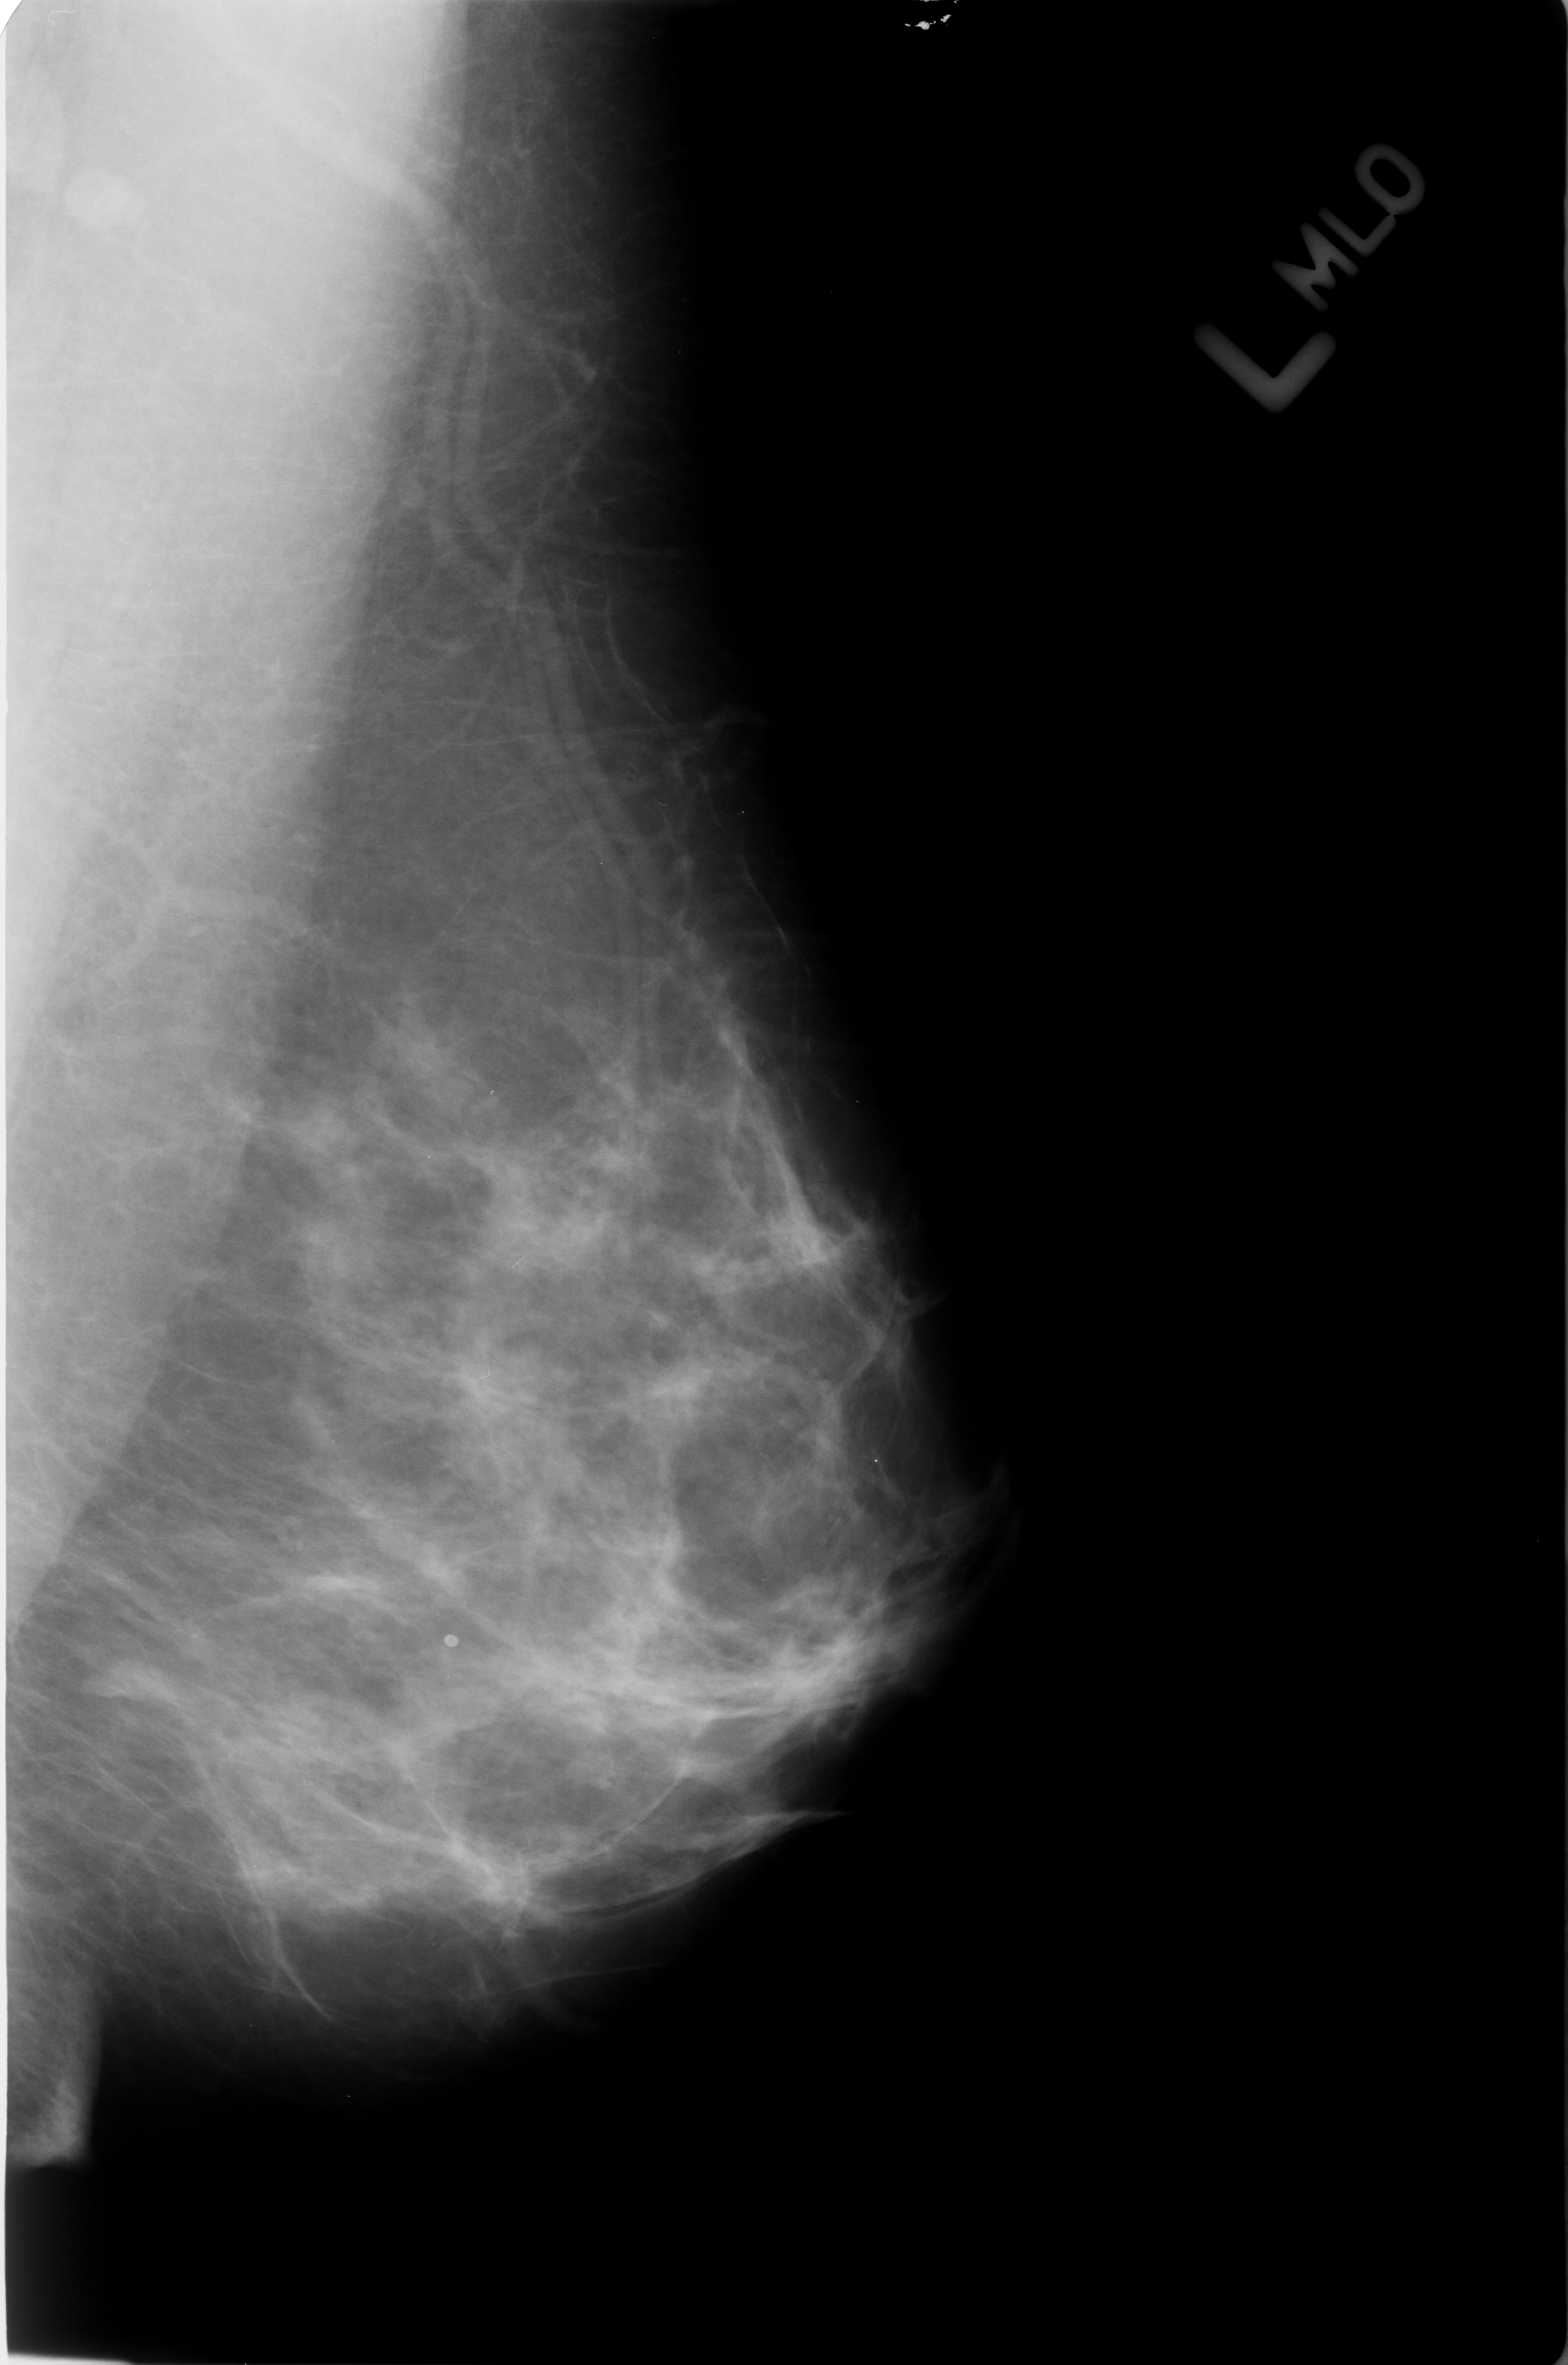
Mammogram (digitized film). Left breast. MLO view. Breast composition: heterogeneously dense (BI-RADS density category 3 of 4). 1568 × 2365 image matrix.
Marked abnormalities (boxes around the expert regions of interest):
- calcifications, morphology lucent center; BI-RADS assessment category 2; outcome (as recorded, no biopsy): benign without callback (not worked up further): bounding box <406,1597,495,1686> (left, top, right, bottom; pixels)